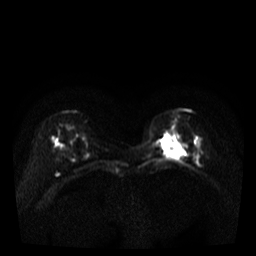
Breast MRI, one axial slice; slice 11 of 35 in the series (ordered by position); diffusion-weighted series; image 2 of 4 stored at this slice position (different b-values; order by instance number); 3 T; 256 × 256 image matrix, field of view 320 × 320 mm. Female patient.
Annotated regions visible in this slice (outlined manually by an expert reader):
- tumour on diffusion-weighted imaging: bounding box [x1, y1, x2, y2] px = [165, 140, 184, 159]